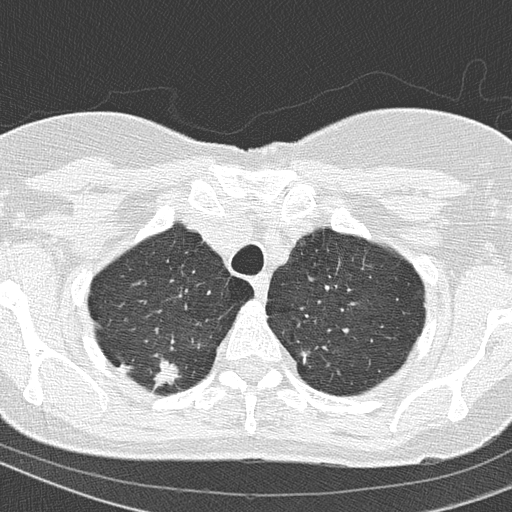
Low-dose screening chest CT, one axial slice. Slice 131 of 154 in the series (ordered by position). 120 kVp. Lung window (W 1500 / L -600 HU). 2 mm slice thickness. 512 × 512 image matrix.
Structures marked on this image (manually delineated by an expert):
- lesion 1 (tumor, upper lobe of right lung): bounding box (x1, y1, x2, y2) in pixels: (153, 358, 181, 387)